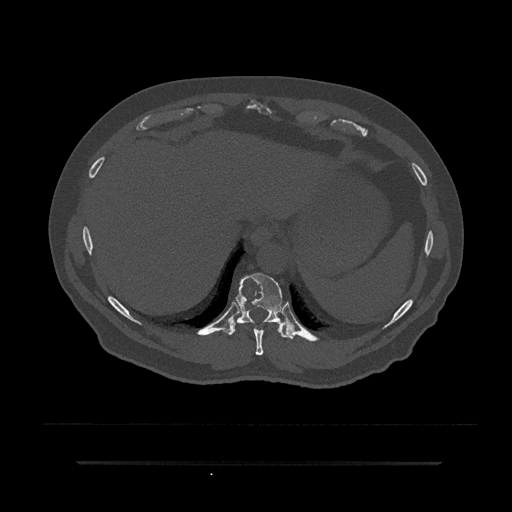
CT including the spine, one axial slice; position 347 of 797 along the scan axis; reconstruction kernel Br40s/3; bone window (W 1800 / L 400 HU); 0.5 mm slice thickness; 512 × 512 image matrix. Patient: male, 59 years. Case-level facts recorded for this patient, not image findings: primary cancer: bile ducts; vertebrae with lytic lesions (as recorded): T10.
Annotated regions visible in this slice (semi-automatic segmentation, software-assisted and operator-edited):
- T10 vertebra: bounding box (x1, y1, x2, y2) in pixels: (227, 273, 294, 339)
- T9 vertebra: (254, 328, 264, 355)